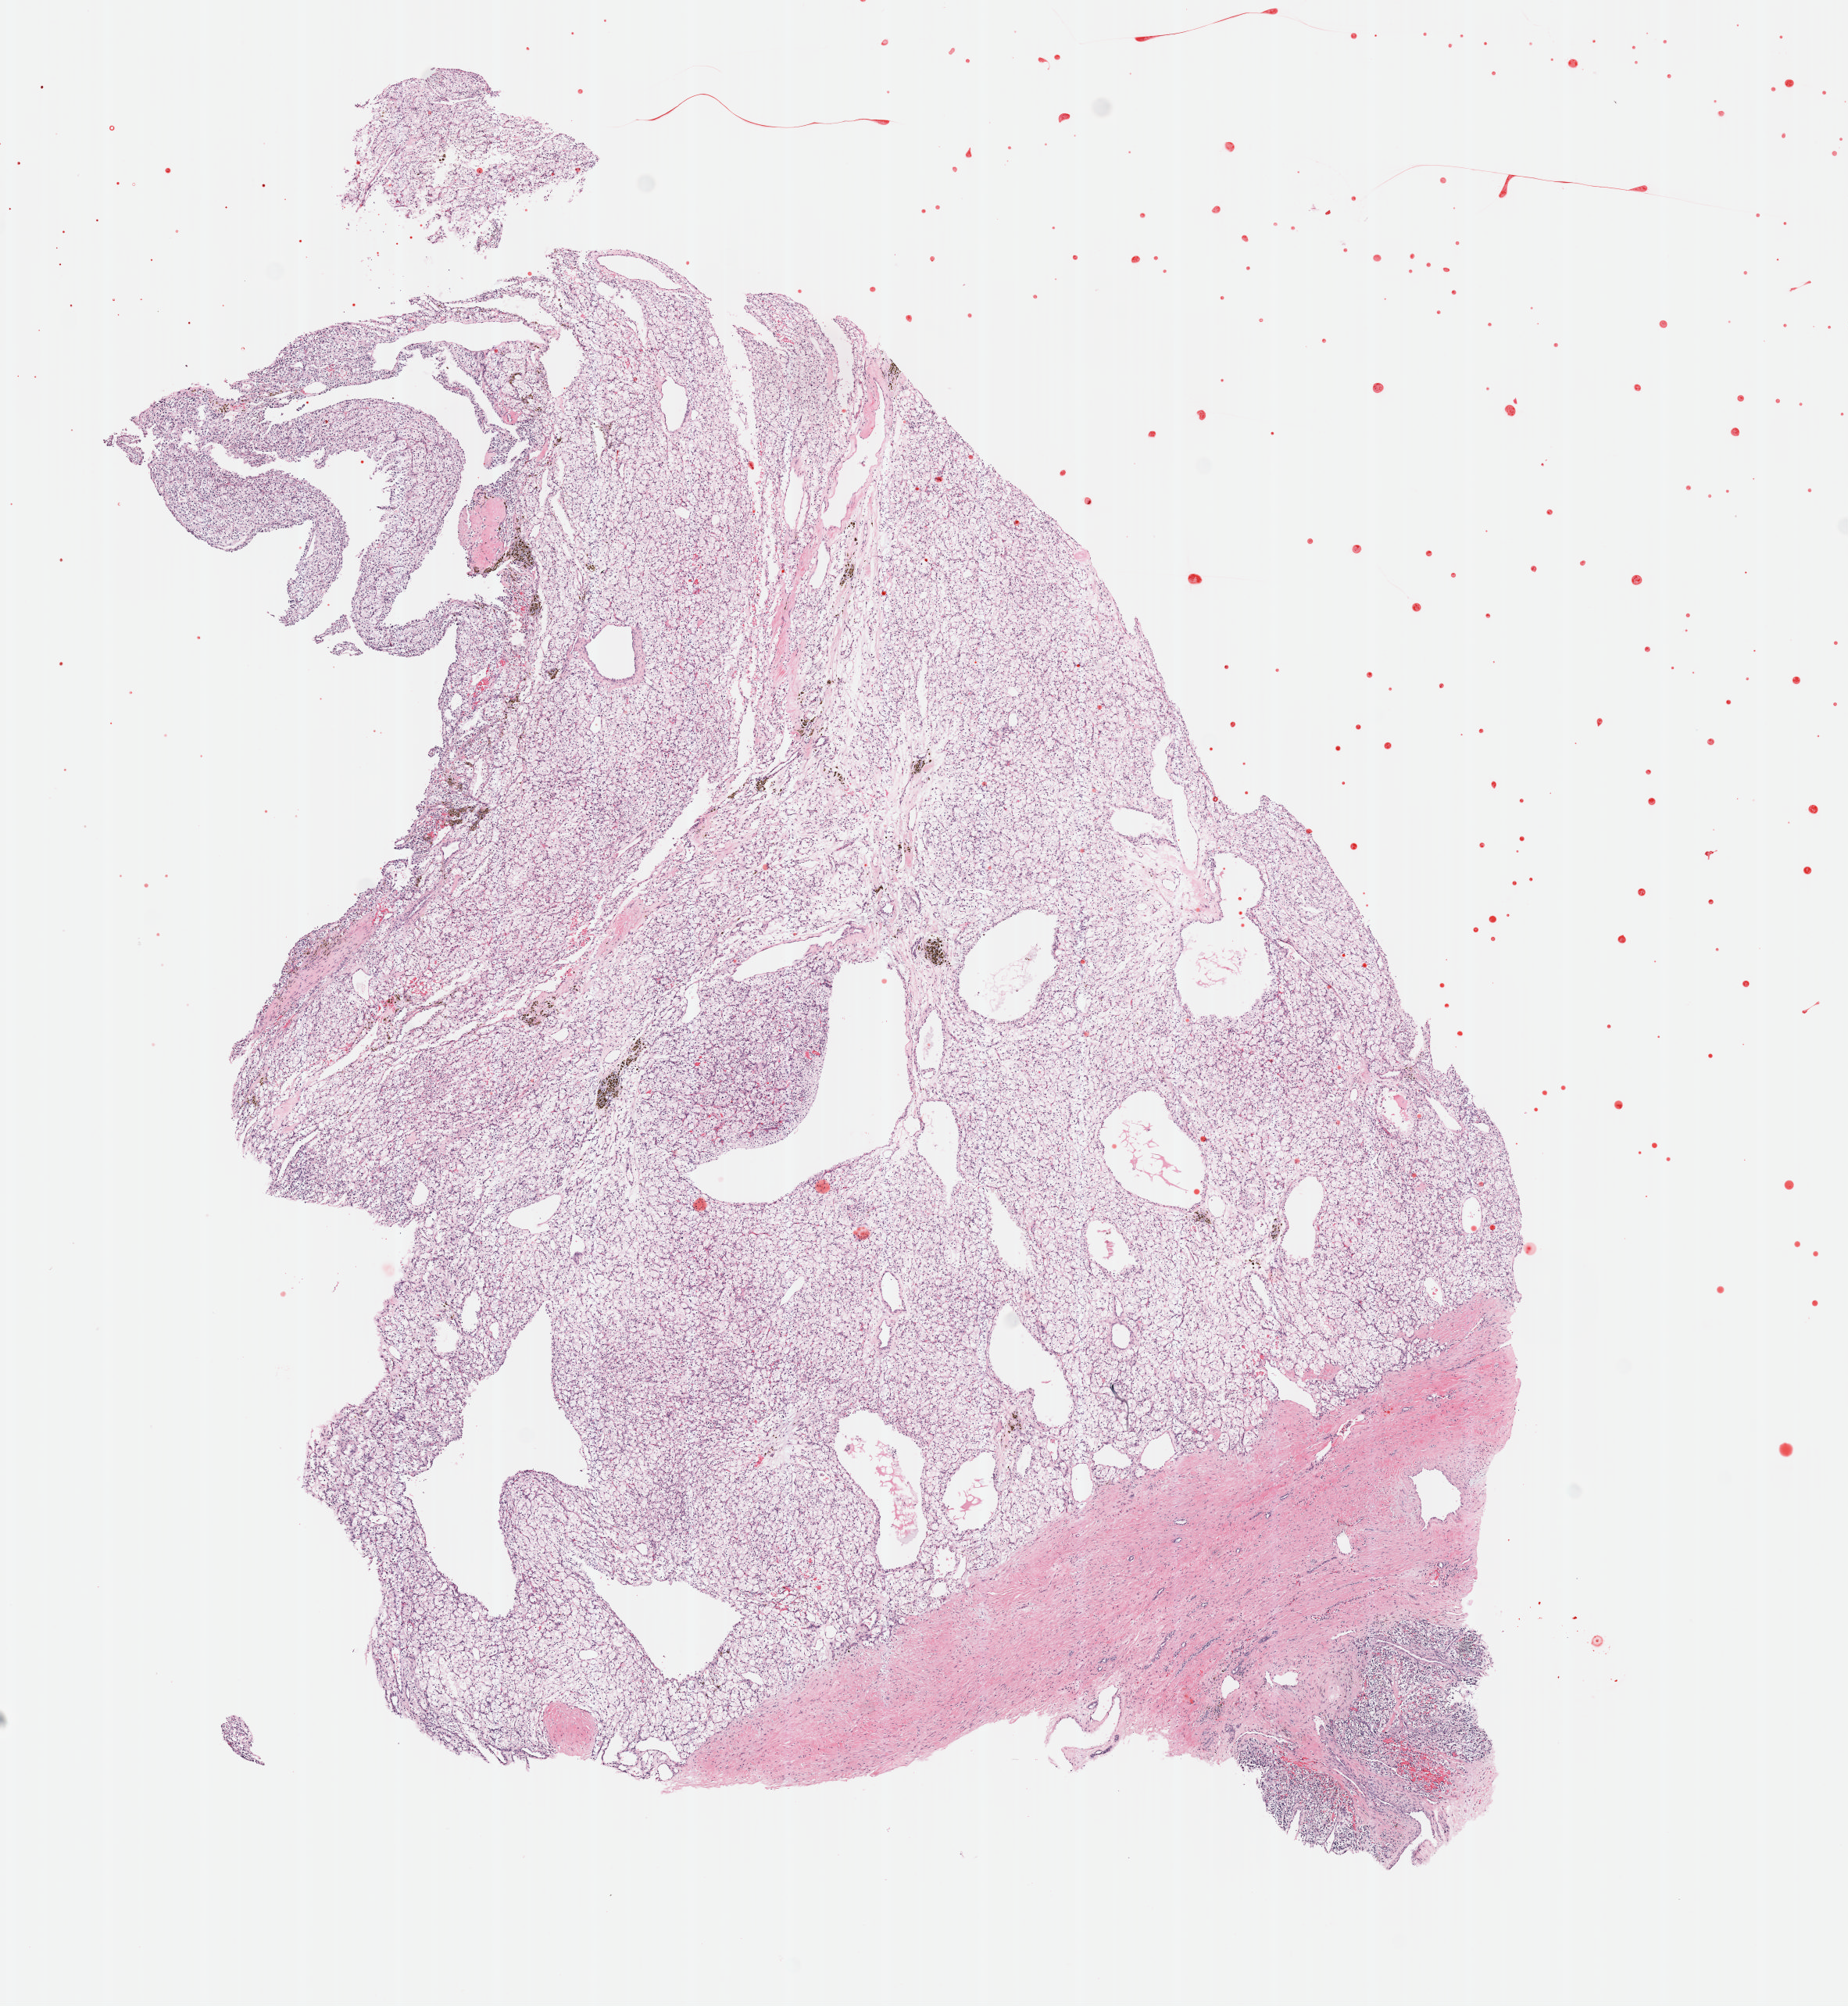
Whole-slide histology image, H&E-stained, shown as a low-resolution overview of the whole scanned area (about 9.6 x 10.4 mm); FFPE section; sample: primary tumour, kidney. Patient: male, age at initial diagnosis 58 years. Histologic grade: G2 (moderately differentiated).
* diagnosis: Clear cell adenocarcinoma, NOS
* AJCC pathologic stage: I